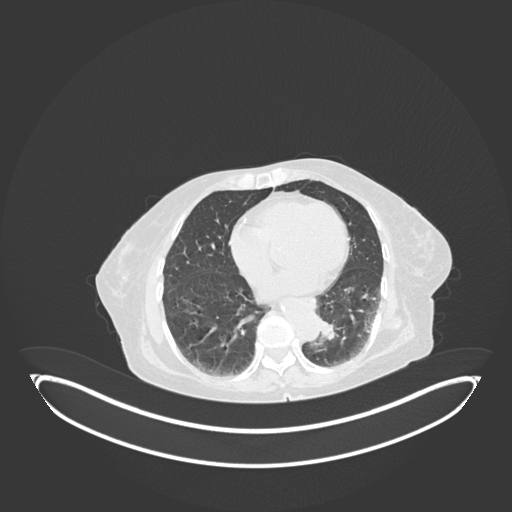
Chest CT, one axial slice. Position 30 of 189 along the scan axis. 120 kVp. Lung window (W 1500 / L -600 HU). 1 mm slice thickness. 512 × 512 image matrix, field of view 500 × 500 mm. Female patient, age 82 years. From the clinical record (not read from this slice): clinical TNM (as recorded): T1b N0 M1.
Structures marked on this image (rectangle marked by the reading radiologist):
- lung tumour (recorded histology: adenocarcinoma): box from (x=320, y=314) to (x=340, y=346) px